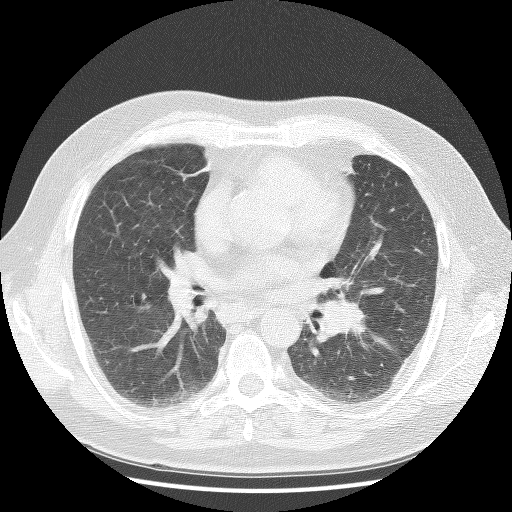
Chest CT (low-dose screening protocol), one axial image, baseline annual screen, lung window (W 1500 / L -600 HU), 2.5 mm slice thickness. Male participant, aged 59 years at enrolment. Current smoker at enrolment.
Expert reader's lesion annotation, bounding box (x1, y1, x2, y2) in pixels: (303, 287, 378, 361). Reader record for this screening exam (exam-level; its link to the box is not recorded): non-calcified nodule or mass ≥4 mm, right upper lobe, 4 × 4 mm, soft tissue attenuation. Note: the box lies in the patient's left hemithorax on this image, whereas the reader's record names the right lung; they may be different findings. Official screen result: positive, change unspecified: nodule(s) >= 4 mm or enlarging nodule(s), mass(es), or other non-specific abnormalities suspicious for lung cancer.